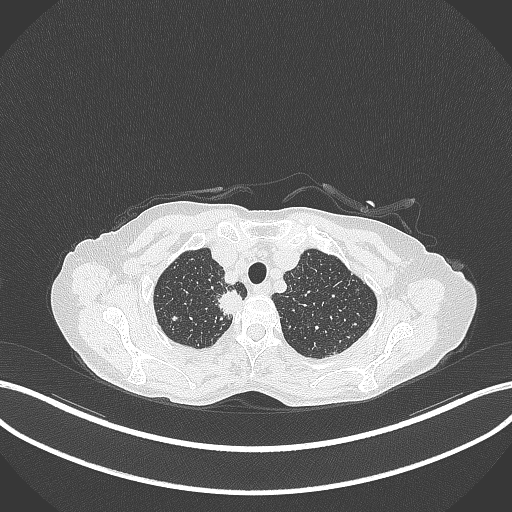
Chest CT, one axial slice. Position 321 of 403 along the scan axis. Reconstruction kernel B70f. 120 kVp. Lung window (W 1500 / L -600 HU). 1 mm slice thickness. 512 × 512 image matrix. Patient: female, 75 years. Case-level facts recorded for this patient, not image findings: clinical TNM (as recorded): T1c N1 M1.
Structures marked on this image (rectangle marked by the reading radiologist):
- lung tumour (recorded histology: adenocarcinoma): box from (x=215, y=289) to (x=247, y=319) px